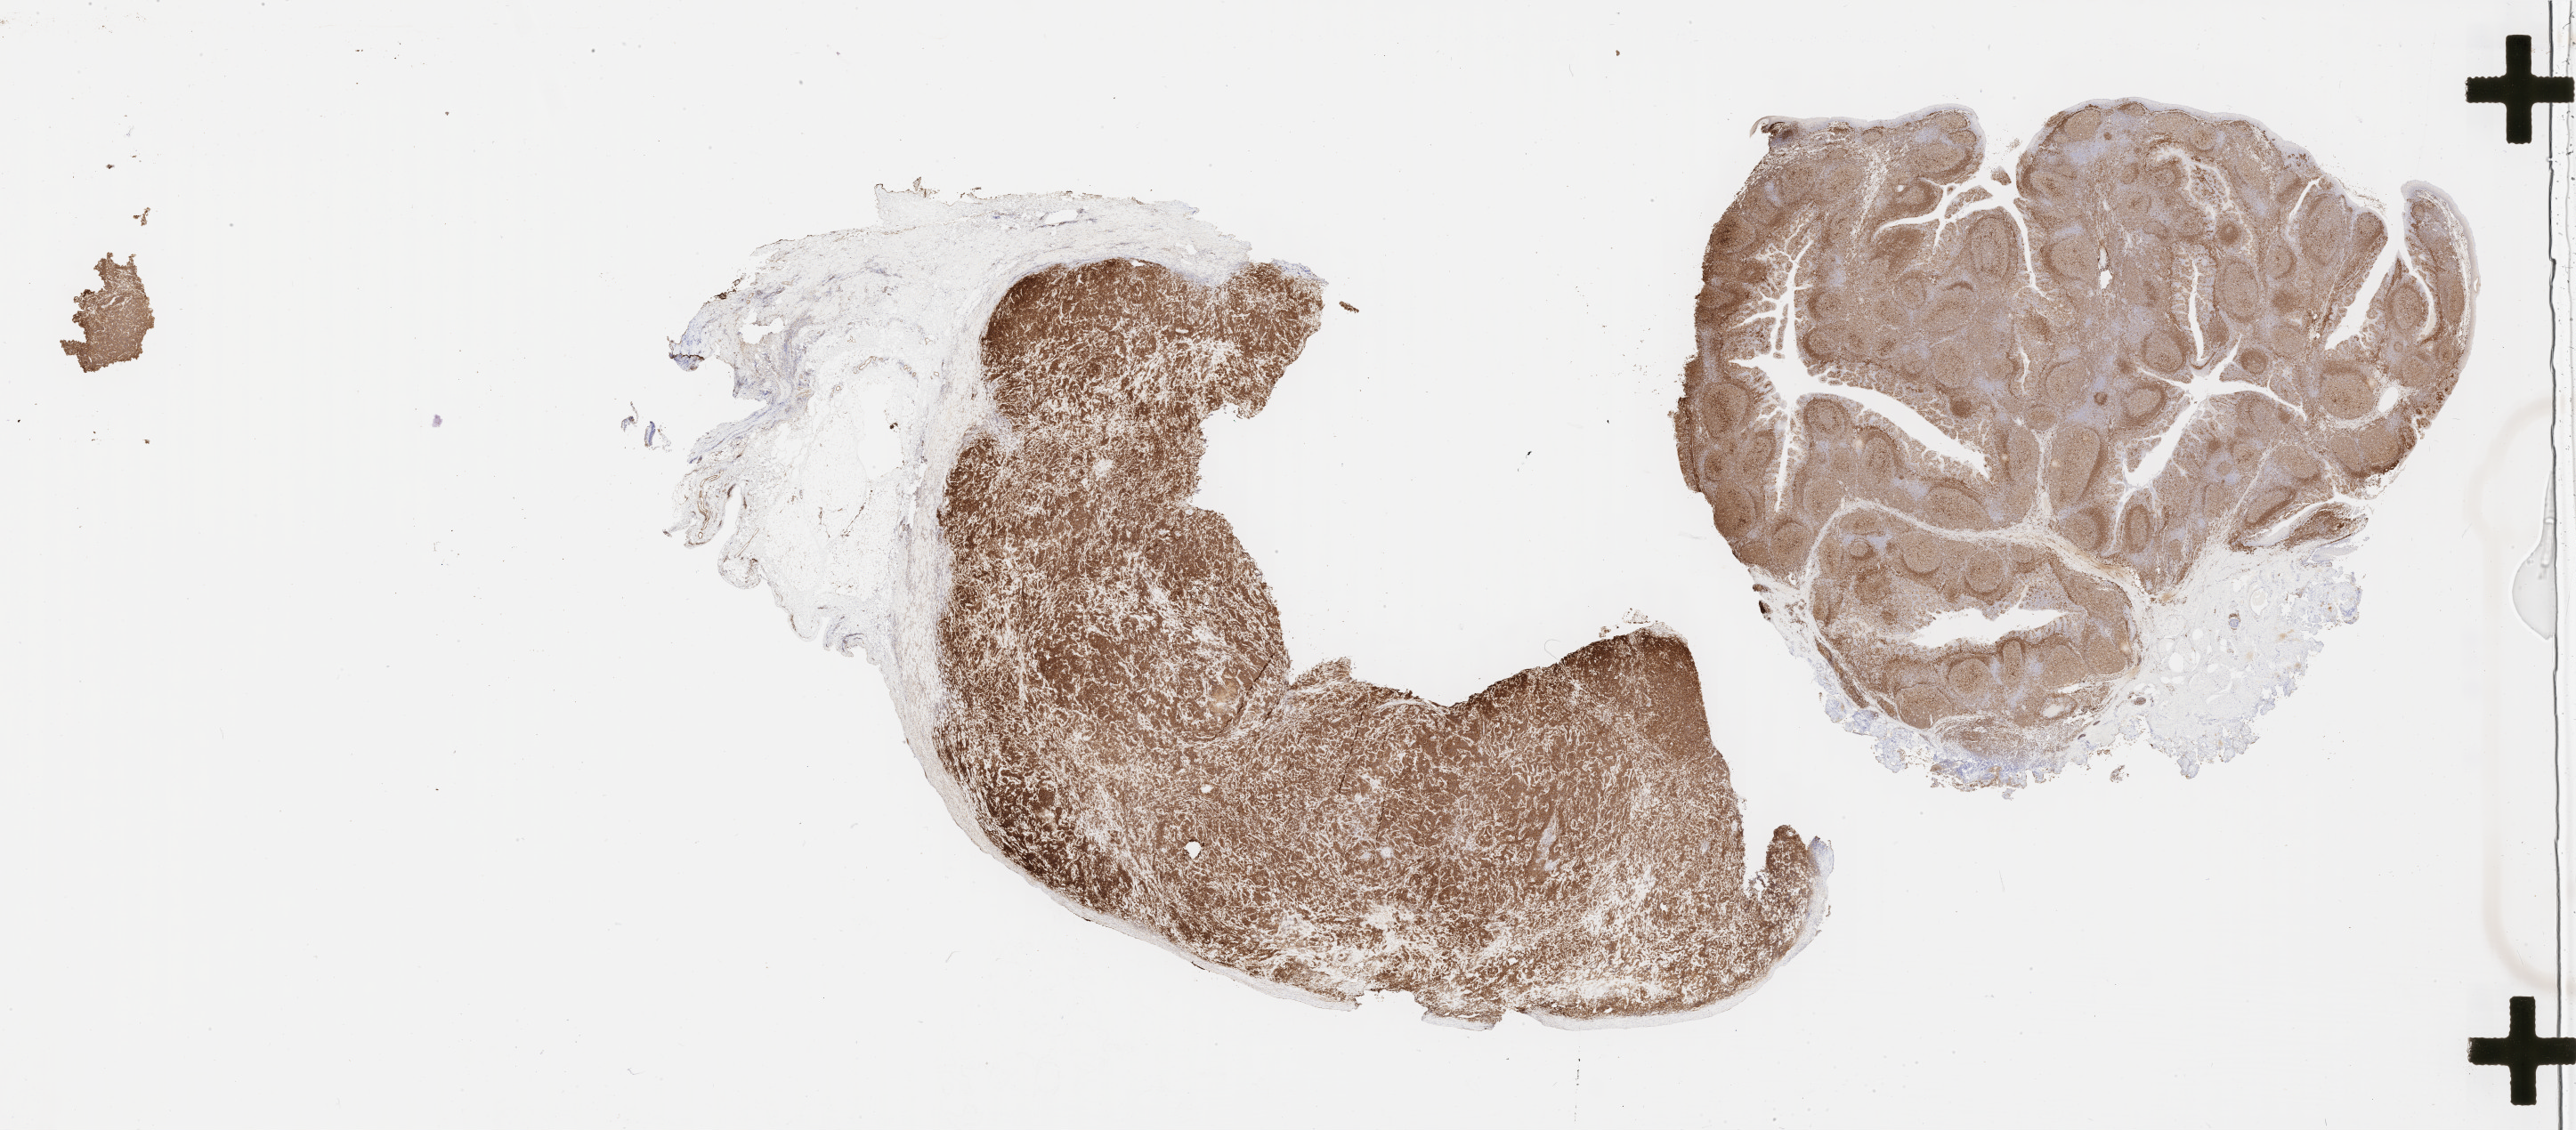
Immunohistochemistry (IHC) whole-slide image stained for CD79a — low-resolution overview of the scanned area, about 46.8 x 20.5 mm. Tumor tissue. Site: bone. Male patient, aged 48.
Diagnosis: Diffuse large B-cell lymphoma, NOS.